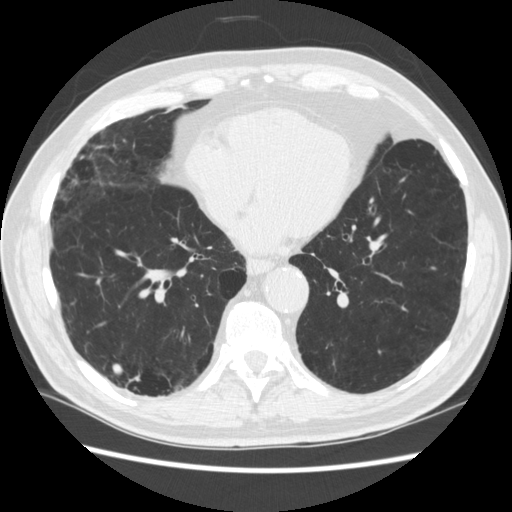
Chest CT (low-dose screening protocol), one axial image. Third annual screen. Lung window (W 1500 / L -600 HU). 1.25 mm slice thickness. Slice 165 of 266 in the series. 512 × 512 image matrix. Male participant, aged 70 years at enrolment.
Expert reader's lesion annotation, bounding box [x1, y1, x2, y2] px = [131, 359, 176, 412]. The screening reader recorded 4 non-calcified nodules or masses ≥4 mm on this exam (right lower lobe, right lower lobe, left lower lobe, left lower lobe); which of them this box marks is not recorded. Lung cancer was diagnosed 253 days after this screen: squamous cell carcinoma, NOS, right upper lobe, poorly differentiated (G3), stage IV (AJCC 6th edition).